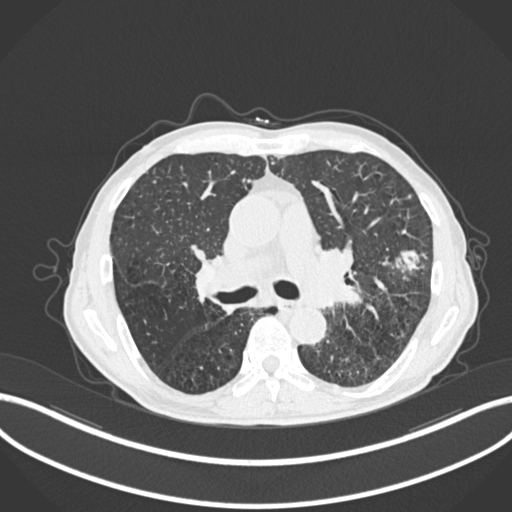
Chest CT, one axial slice. Position 150 of 287 along the scan axis. Reconstruction kernel B30f. 120 kVp. Lung window (W 1500 / L -600 HU). 1 mm slice thickness. 512 × 512 image matrix, field of view 400 × 400 mm. Male patient, age 74 years. From the clinical record (not read from this slice): clinical TNM (as recorded): T2a N1 M0.
Outlined on this slice (rectangle marked by the reading radiologist):
- lung tumour (recorded histology: adenocarcinoma): bounding box [x1, y1, x2, y2] px = [396, 246, 423, 276]